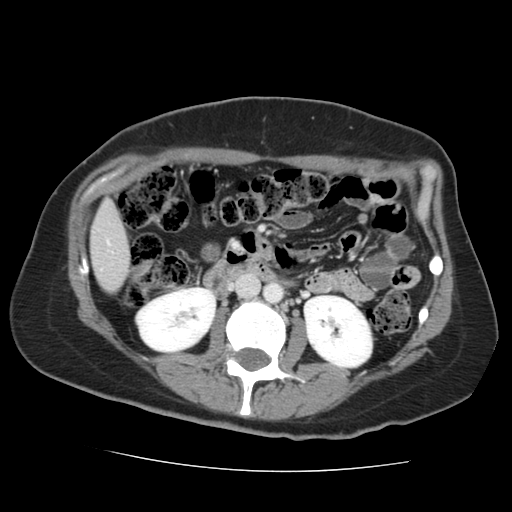
Contrast-enhanced abdominal CT, one axial slice; slice 49 of 144 in the series (ordered by position); 120 kVp; intravenous contrast given; soft-tissue window (W 400 / L 40 HU); 2.5 mm slice thickness; 512 × 512 image matrix, field of view 333 × 333 mm. Female patient, age 46 years. Case-level facts recorded for this patient, not image findings: diagnosis: colorectal cancer liver metastases, imaged before liver resection; multiple liver metastases: no; largest metastasis: 2.8 cm; chemotherapy before resection: yes.
Outlined on this slice (expert manual segmentation):
- liver: bounding box [x1, y1, x2, y2] px = [92, 204, 129, 292]
- planned liver remnant (the part of the liver to remain after resection): [92, 204, 129, 292]